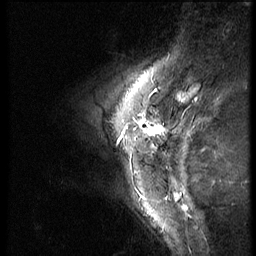
Breast MRI (dynamic contrast-enhanced), one sagittal slice. Position 13 of 56 along the scan axis. Dynamic contrast-enhanced series, image 2 of 3 at this slice position (ordered by acquisition). 1.5 T. TE 4.2 ms, TR 9 ms. 2.5 mm slice thickness. 256 × 256 image matrix, field of view 180 × 180 mm. Patient: female, 46 years. From the clinical record (not read from this slice): setting: breast cancer imaged before/during neoadjuvant chemotherapy; receptor status: HER2-positive.
Annotated regions visible in this slice (semi-automatic segmentation, software-assisted and operator-edited):
- analysis volume of interest (the breast-tissue region the enhancement analysis was run in; not a lesion): bounding box [x1, y1, x2, y2] px = [80, 98, 174, 182]
- tumour enhancement mask (voxels above the 140 % enhancement threshold inside the analysis volume of interest): [122, 117, 158, 137]